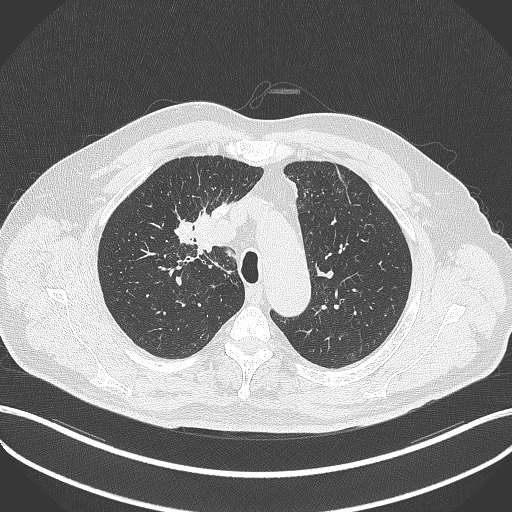
Chest CT, one axial slice; position 297 of 411 along the scan axis; reconstruction kernel B70f; lung window (W 1500 / L -600 HU); 1 mm slice thickness; 512 × 512 image matrix, field of view 400 × 400 mm. Patient: male, 60 years. Case-level facts recorded for this patient, not image findings: clinical TNM (as recorded): T1b N1 M0.
Annotated regions visible in this slice (rectangle marked by the reading radiologist):
- lung tumour (recorded histology: squamous cell carcinoma): bounding box (x1, y1, x2, y2) in pixels: (192, 211, 221, 258)